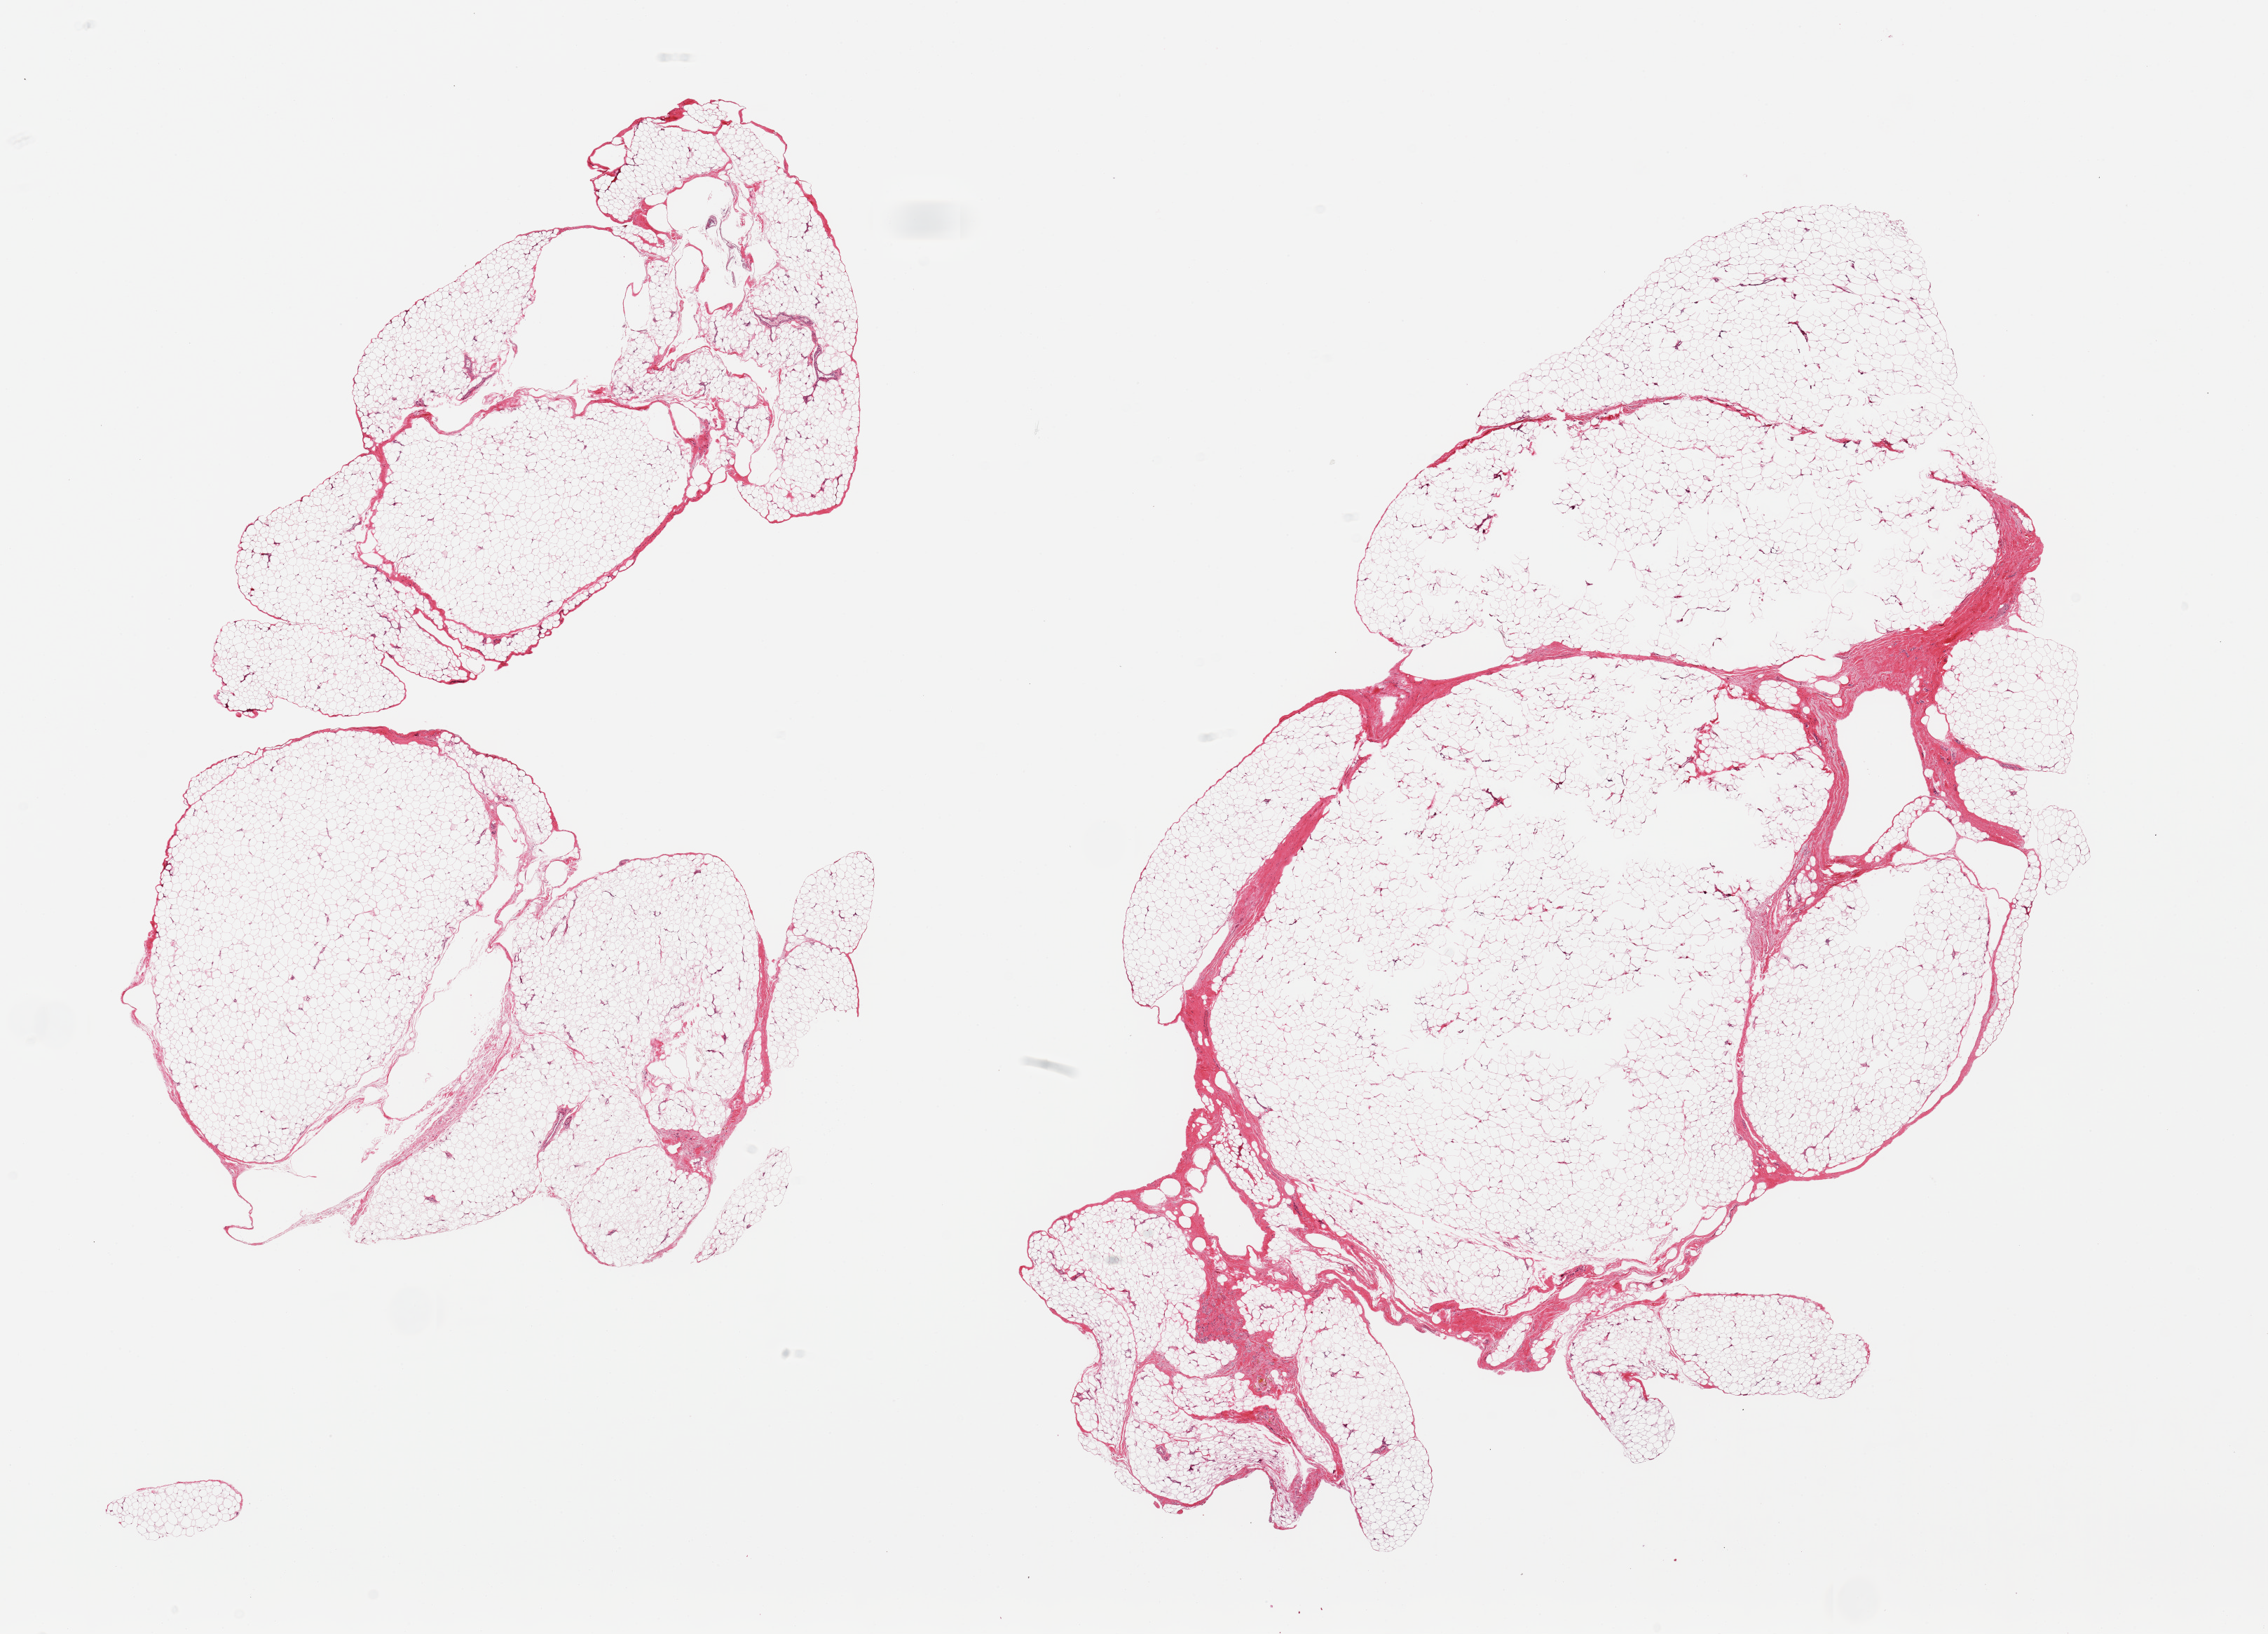
Whole-slide image, haematoxylin and eosin stain — low-resolution overview of the scanned area, about 25.6 x 18.4 mm (from a 20x scan). PAXgene-fixed paraffin-embedded (PFPE) section. Sampled site (target tissue): adipose tissue. Donor tissue sample. Donor sex: male.
• reviewer comment on this tissue sample: 2 pieces